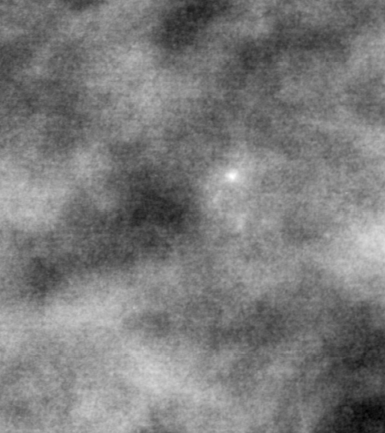
Crop from a digitized film mammogram around one marked abnormality, left breast, MLO view.
Calcifications, morphology pleomorphic, distribution clustered; BI-RADS assessment category 4; subtlety rating 2 on a 1 (subtle) to 5 (obvious) scale; pathology (as recorded): benign.